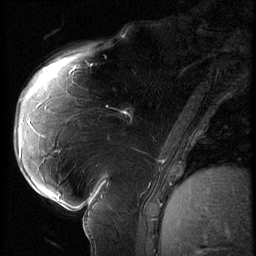
Breast MRI (dynamic contrast-enhanced), one sagittal slice; slice 23 of 62 in the series (ordered by position); 3 images stored at this slice position (order not interpretable as contrast timing); 1.5 T; TE 4.2 ms, TR 9 ms; 256 × 256 image matrix. Patient: female, 57 years. Case-level facts recorded for this patient, not image findings: setting: breast cancer imaged before/during neoadjuvant chemotherapy; receptor status: triple-negative.
Outlined on this slice (semi-automatically segmented with operator editing):
- analysis volume of interest (the breast-tissue region the enhancement analysis was run in; not a lesion): bounding box (x1, y1, x2, y2) in pixels: (105, 84, 158, 135)
- tumour enhancement mask (voxels above the 140 % enhancement threshold inside the analysis volume of interest): (122, 110, 128, 115)